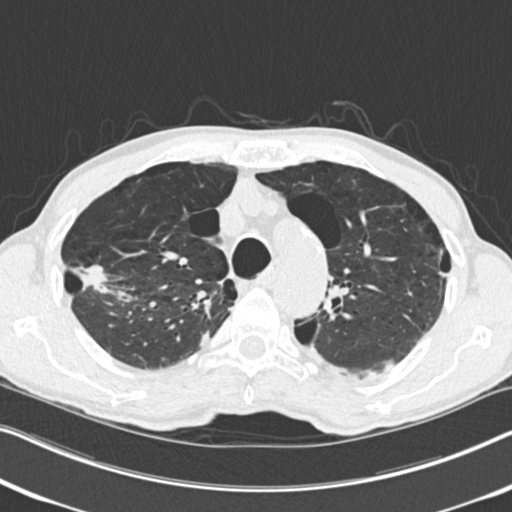
Axial slice from a low-dose chest CT screening exam, second annual screen, lung window (W 1500 / L -600 HU), 2 mm slice thickness, standard (soft-tissue) reconstruction kernel (B30f). Male, age 71 years at enrolment.
Lesion marked by an expert reader, bounding box <63,244,135,318> (left, top, right, bottom; pixels). The screening reader recorded 4 non-calcified nodules or masses ≥4 mm on this exam (right upper lobe, right upper lobe, right upper lobe, left upper lobe); which of them this box marks is not recorded. Official screen result: positive, change unspecified: nodule(s) >= 4 mm or enlarging nodule(s), mass(es), or other non-specific abnormalities suspicious for lung cancer. Participant outcome: lung cancer diagnosed 83 days after this screen — adenocarcinoma, NOS, right upper lobe, well differentiated (G1), stage IA (AJCC 6th edition), 30 mm at pathology.